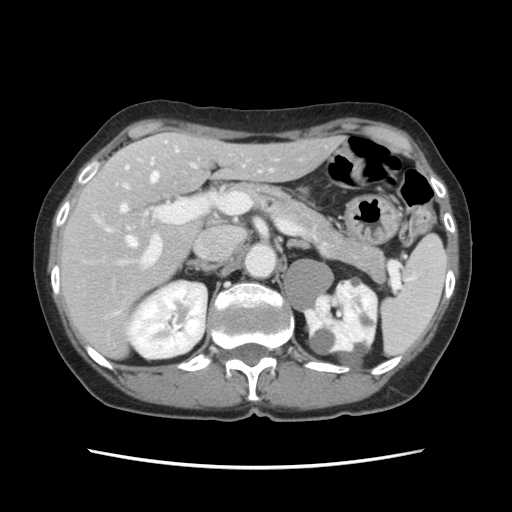
Contrast-enhanced abdominal CT, one axial slice; position 75 of 120 along the scan axis; soft-tissue window (W 400 / L 40 HU); 2.5 mm slice thickness; 512 × 512 image matrix, field of view 330 × 330 mm. Female patient, age 70 years. Case-level facts recorded for this patient, not image findings: diagnosis: colorectal cancer liver metastases, imaged before liver resection; multiple liver metastases: no; largest metastasis: 2.5 cm; chemotherapy before resection: yes.
Annotated regions visible in this slice (outlined manually by an expert reader):
- hepatic veins: bounding box (x1, y1, x2, y2) in pixels: (106, 149, 178, 247)
- liver: (61, 133, 339, 356)
- planned liver remnant (the part of the liver to remain after resection): (92, 133, 339, 284)
- portal vein (with intrahepatic branches): (116, 141, 232, 314)